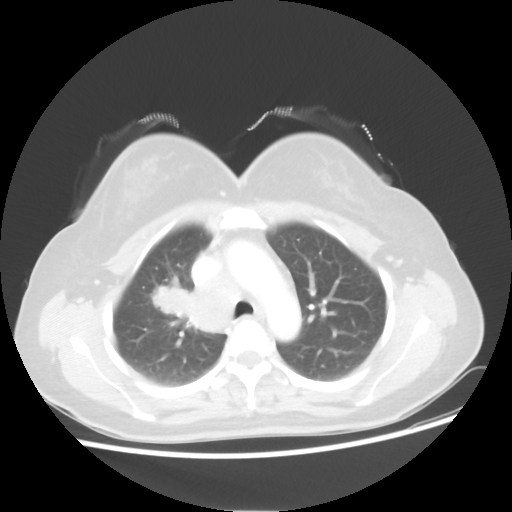
Chest CT, one axial slice. Reconstruction kernel STANDARD. Lung window (W 1500 / L -600 HU). 512 × 512 image matrix, field of view 360 × 360 mm. Female patient, age 40 years. Case-level facts recorded for this patient, not image findings: clinical TNM (as recorded): T1c N3 M0; histopathological grade: G3.
Structures marked on this image (bounding box drawn by a radiologist):
- lung tumour (recorded histology: small cell carcinoma): bounding box (x1, y1, x2, y2) in pixels: (151, 278, 190, 317)